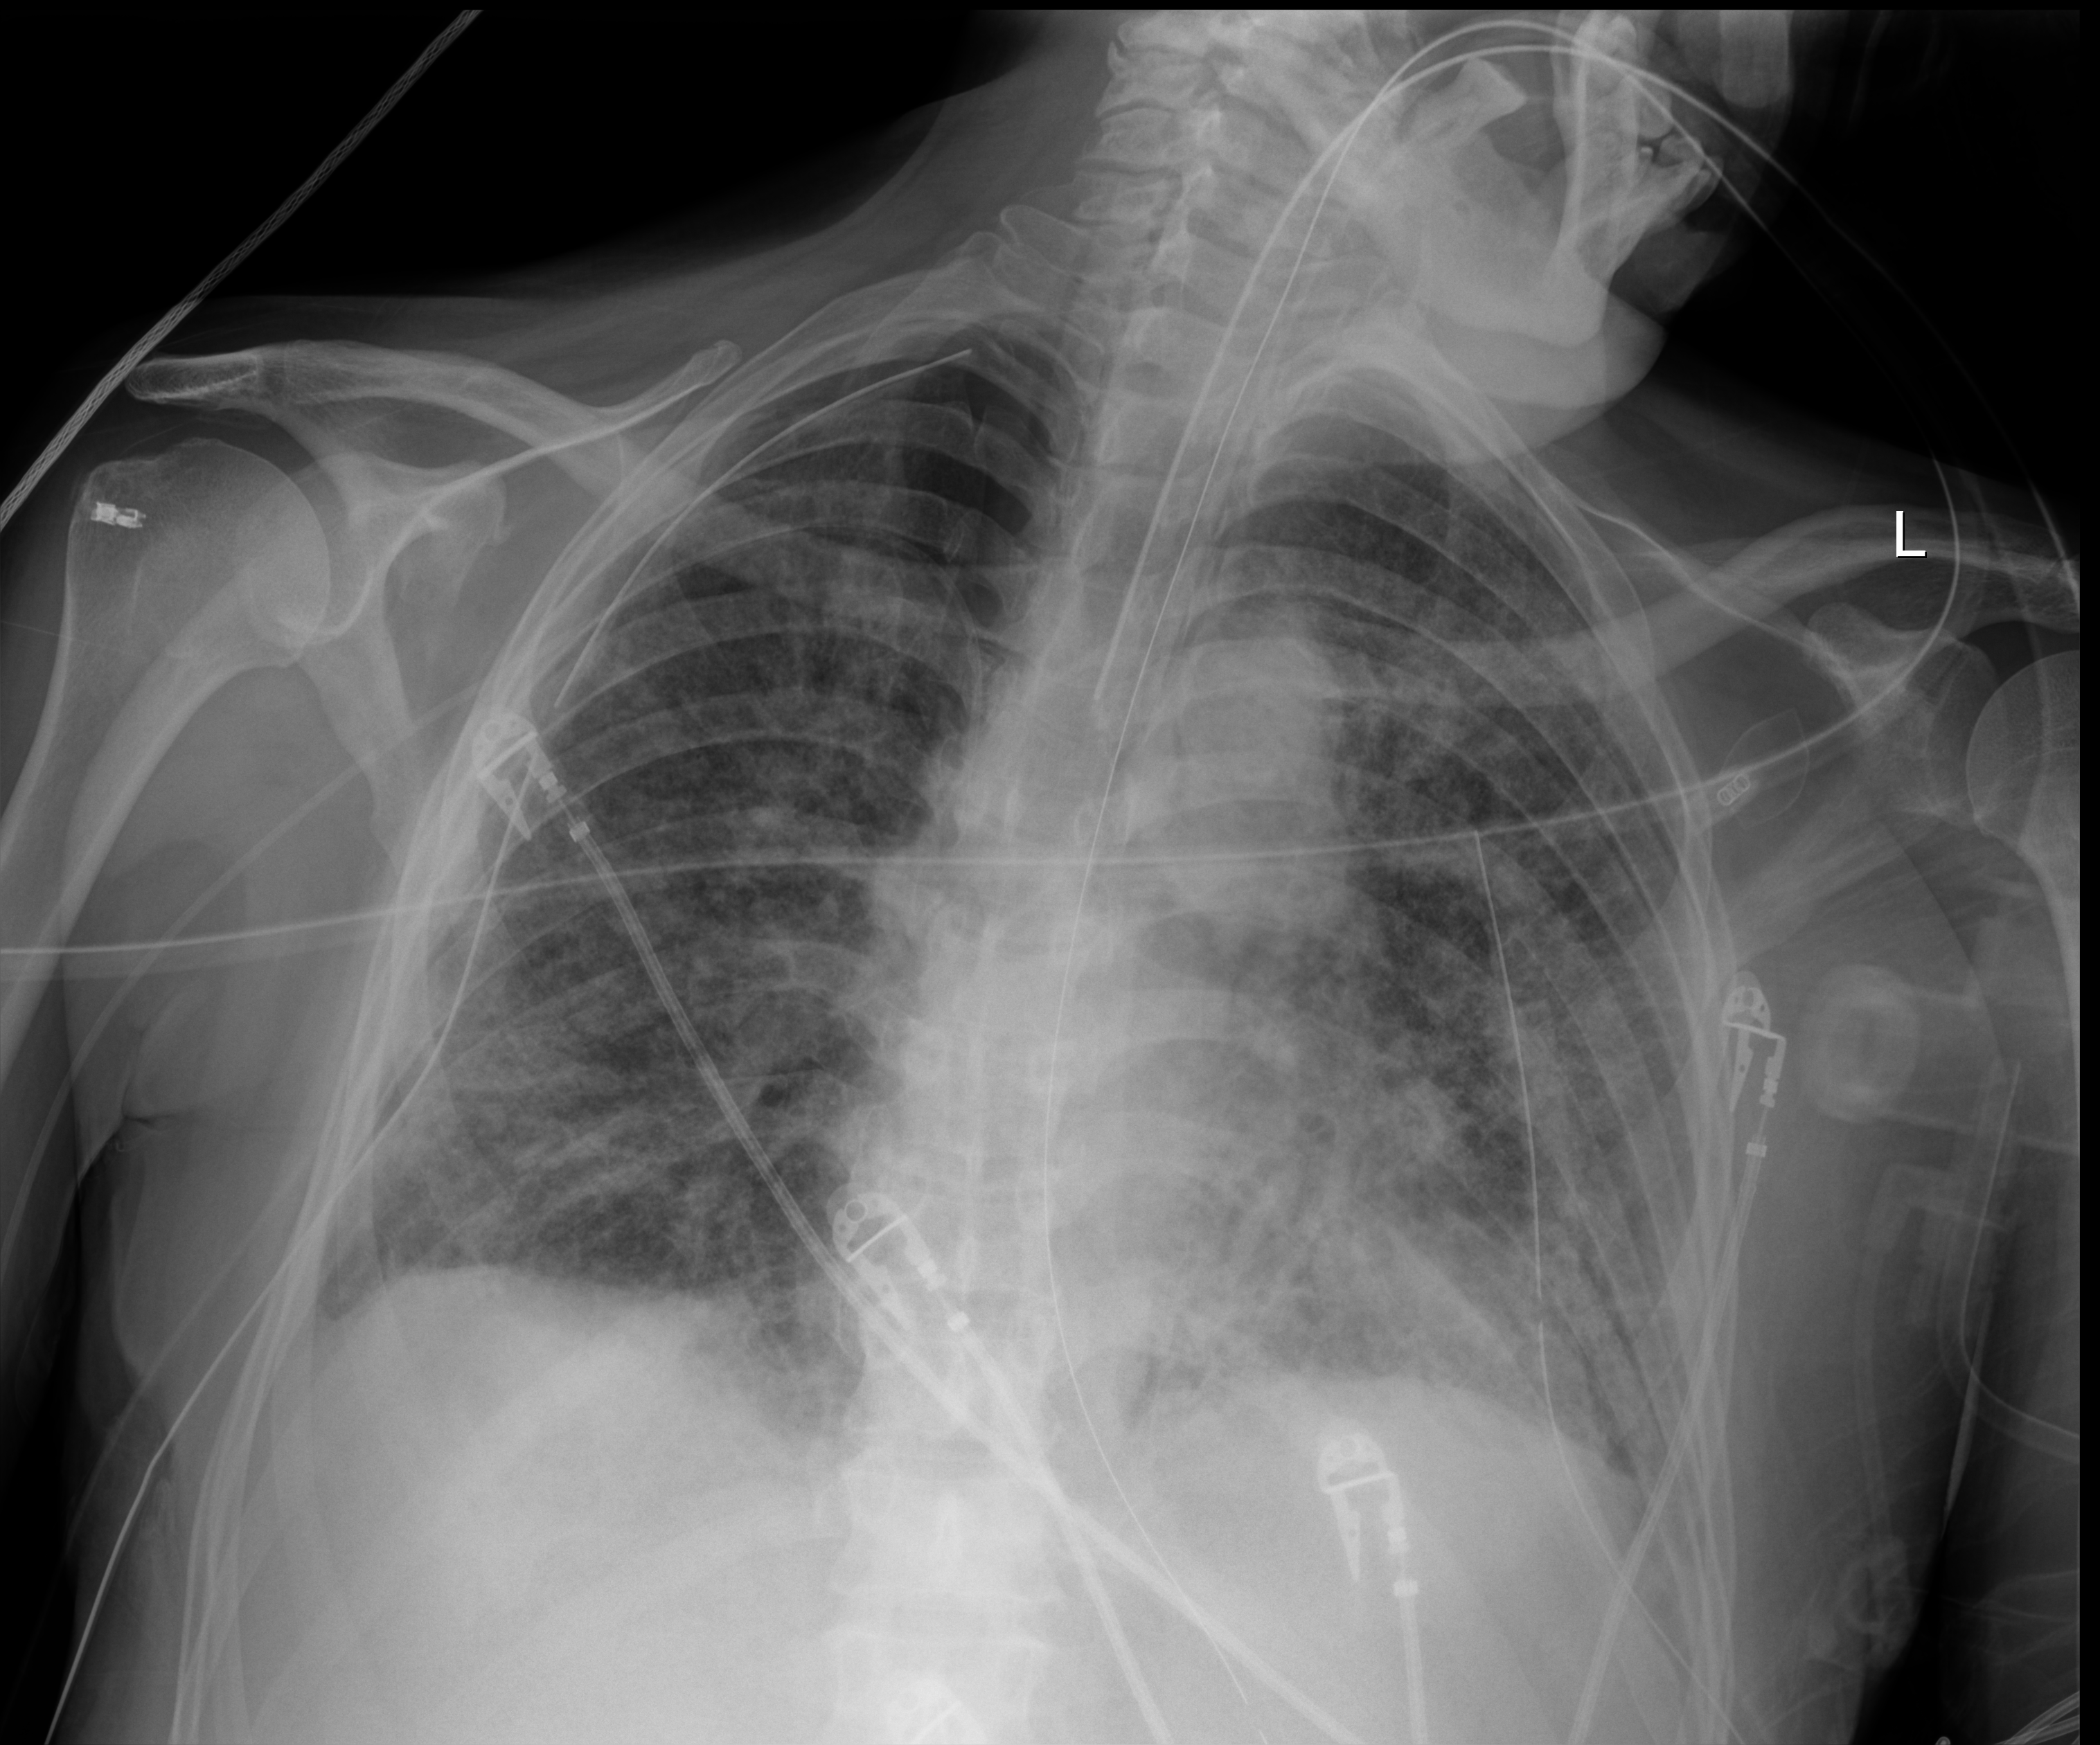
Chest X-ray, anteroposterior (AP) projection. Male patient hospitalised with COVID-19, age 60–74 years.
Admission-level facts for this patient (not findings on this image; timing relative to this image not recorded): smoking status (admission record): never; mechanically ventilated during this hospital stay: yes.